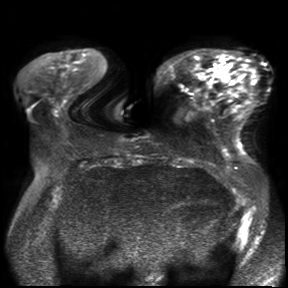
Breast MRI, one axial slice. Slice 9 of 30 in the series (ordered by position). Diffusion-weighted series; image 2 of 4 stored at this slice position (different b-values; order by instance number). 3 T. 4 mm slice thickness. 288 × 288 image matrix, field of view 360 × 360 mm. Female patient.
Annotated regions visible in this slice (outlined manually by an expert reader):
- tumour on diffusion-weighted imaging: bounding box <216,63,232,81> (left, top, right, bottom; pixels)